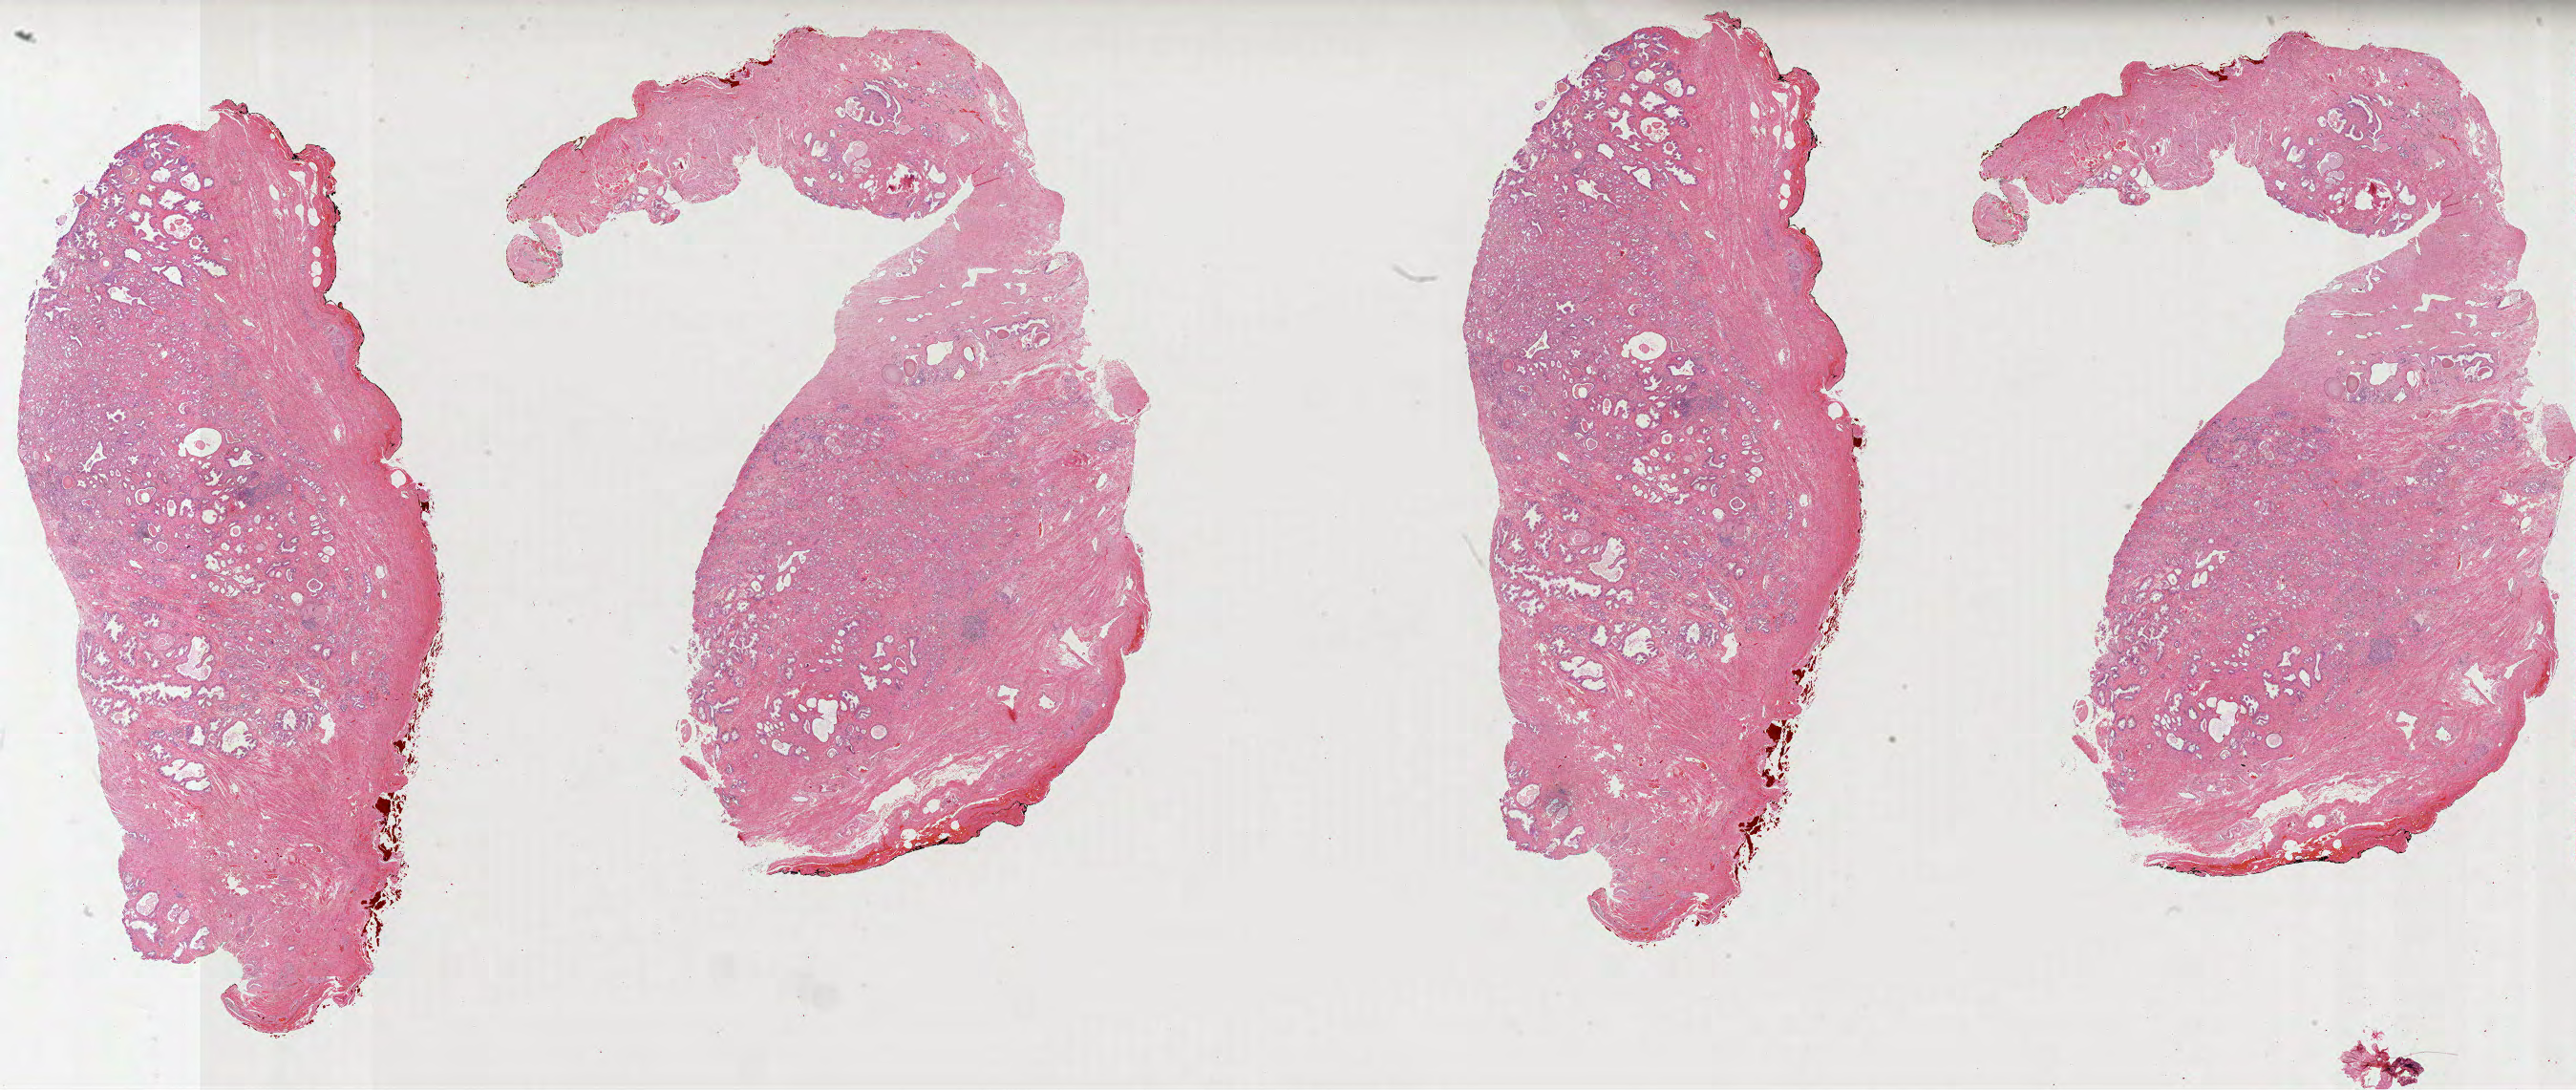
Whole-slide histology image, Hematoxylin and eosin (H&E) stained, shown as a low-resolution overview of the whole scanned area (about 43.5 x 18.4 mm, slide scanned at 40x), formalin-fixed paraffin-embedded (FFPE) diagnostic section, prostate, primary tumour sample. Male patient; age at initial diagnosis 58 years. Gleason score: 7 (3+4).
Histologic diagnosis: Acinar cell carcinoma (prostate gland).